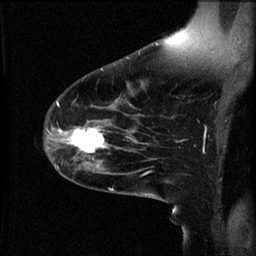
Breast MRI (dynamic contrast-enhanced), one sagittal slice; slice 37 of 60 in the series (ordered by position); 3 images stored at this slice position (order not interpretable as contrast timing); 1.5 T; TE 4.2 ms, TR 8.2 ms; 2 mm slice thickness; 256 × 256 image matrix, field of view 200 × 200 mm. Female patient, age 49 years.
Outlined on this slice (semi-automatic segmentation, software-assisted and operator-edited):
- analysis volume of interest (the breast-tissue region the enhancement analysis was run in; not a lesion): bounding box (x1, y1, x2, y2) in pixels: (66, 124, 113, 159)
- tumour enhancement mask (voxels above the 70 % enhancement threshold inside the analysis volume of interest): (66, 128, 109, 153)